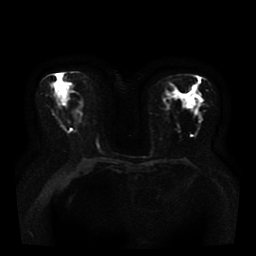
Breast MRI, one axial slice. Position 17 of 36 along the scan axis. Diffusion-weighted series; image 2 of 4 stored at this slice position (different b-values; order by instance number). 1.5 T. 5 mm slice thickness. 256 × 256 image matrix. Female patient.
Annotated regions visible in this slice (outlined manually by an expert reader):
- tumour on diffusion-weighted imaging: bounding box (x1, y1, x2, y2) in pixels: (188, 95, 203, 106)